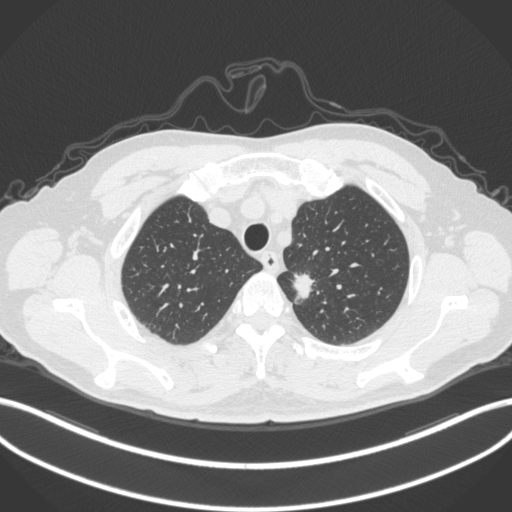
Chest CT, one axial slice. Position 312 of 382 along the scan axis. Reconstruction kernel B31f. 120 kVp. Lung window (W 1500 / L -600 HU). 1 mm slice thickness. 512 × 512 image matrix, field of view 400 × 400 mm. Patient: male, 64 years. Case-level facts recorded for this patient, not image findings: clinical TNM (as recorded): T1c N0 M0.
Outlined on this slice (rectangle marked by the reading radiologist):
- lung tumour (recorded histology: adenocarcinoma): bounding box <286,267,317,311> (left, top, right, bottom; pixels)